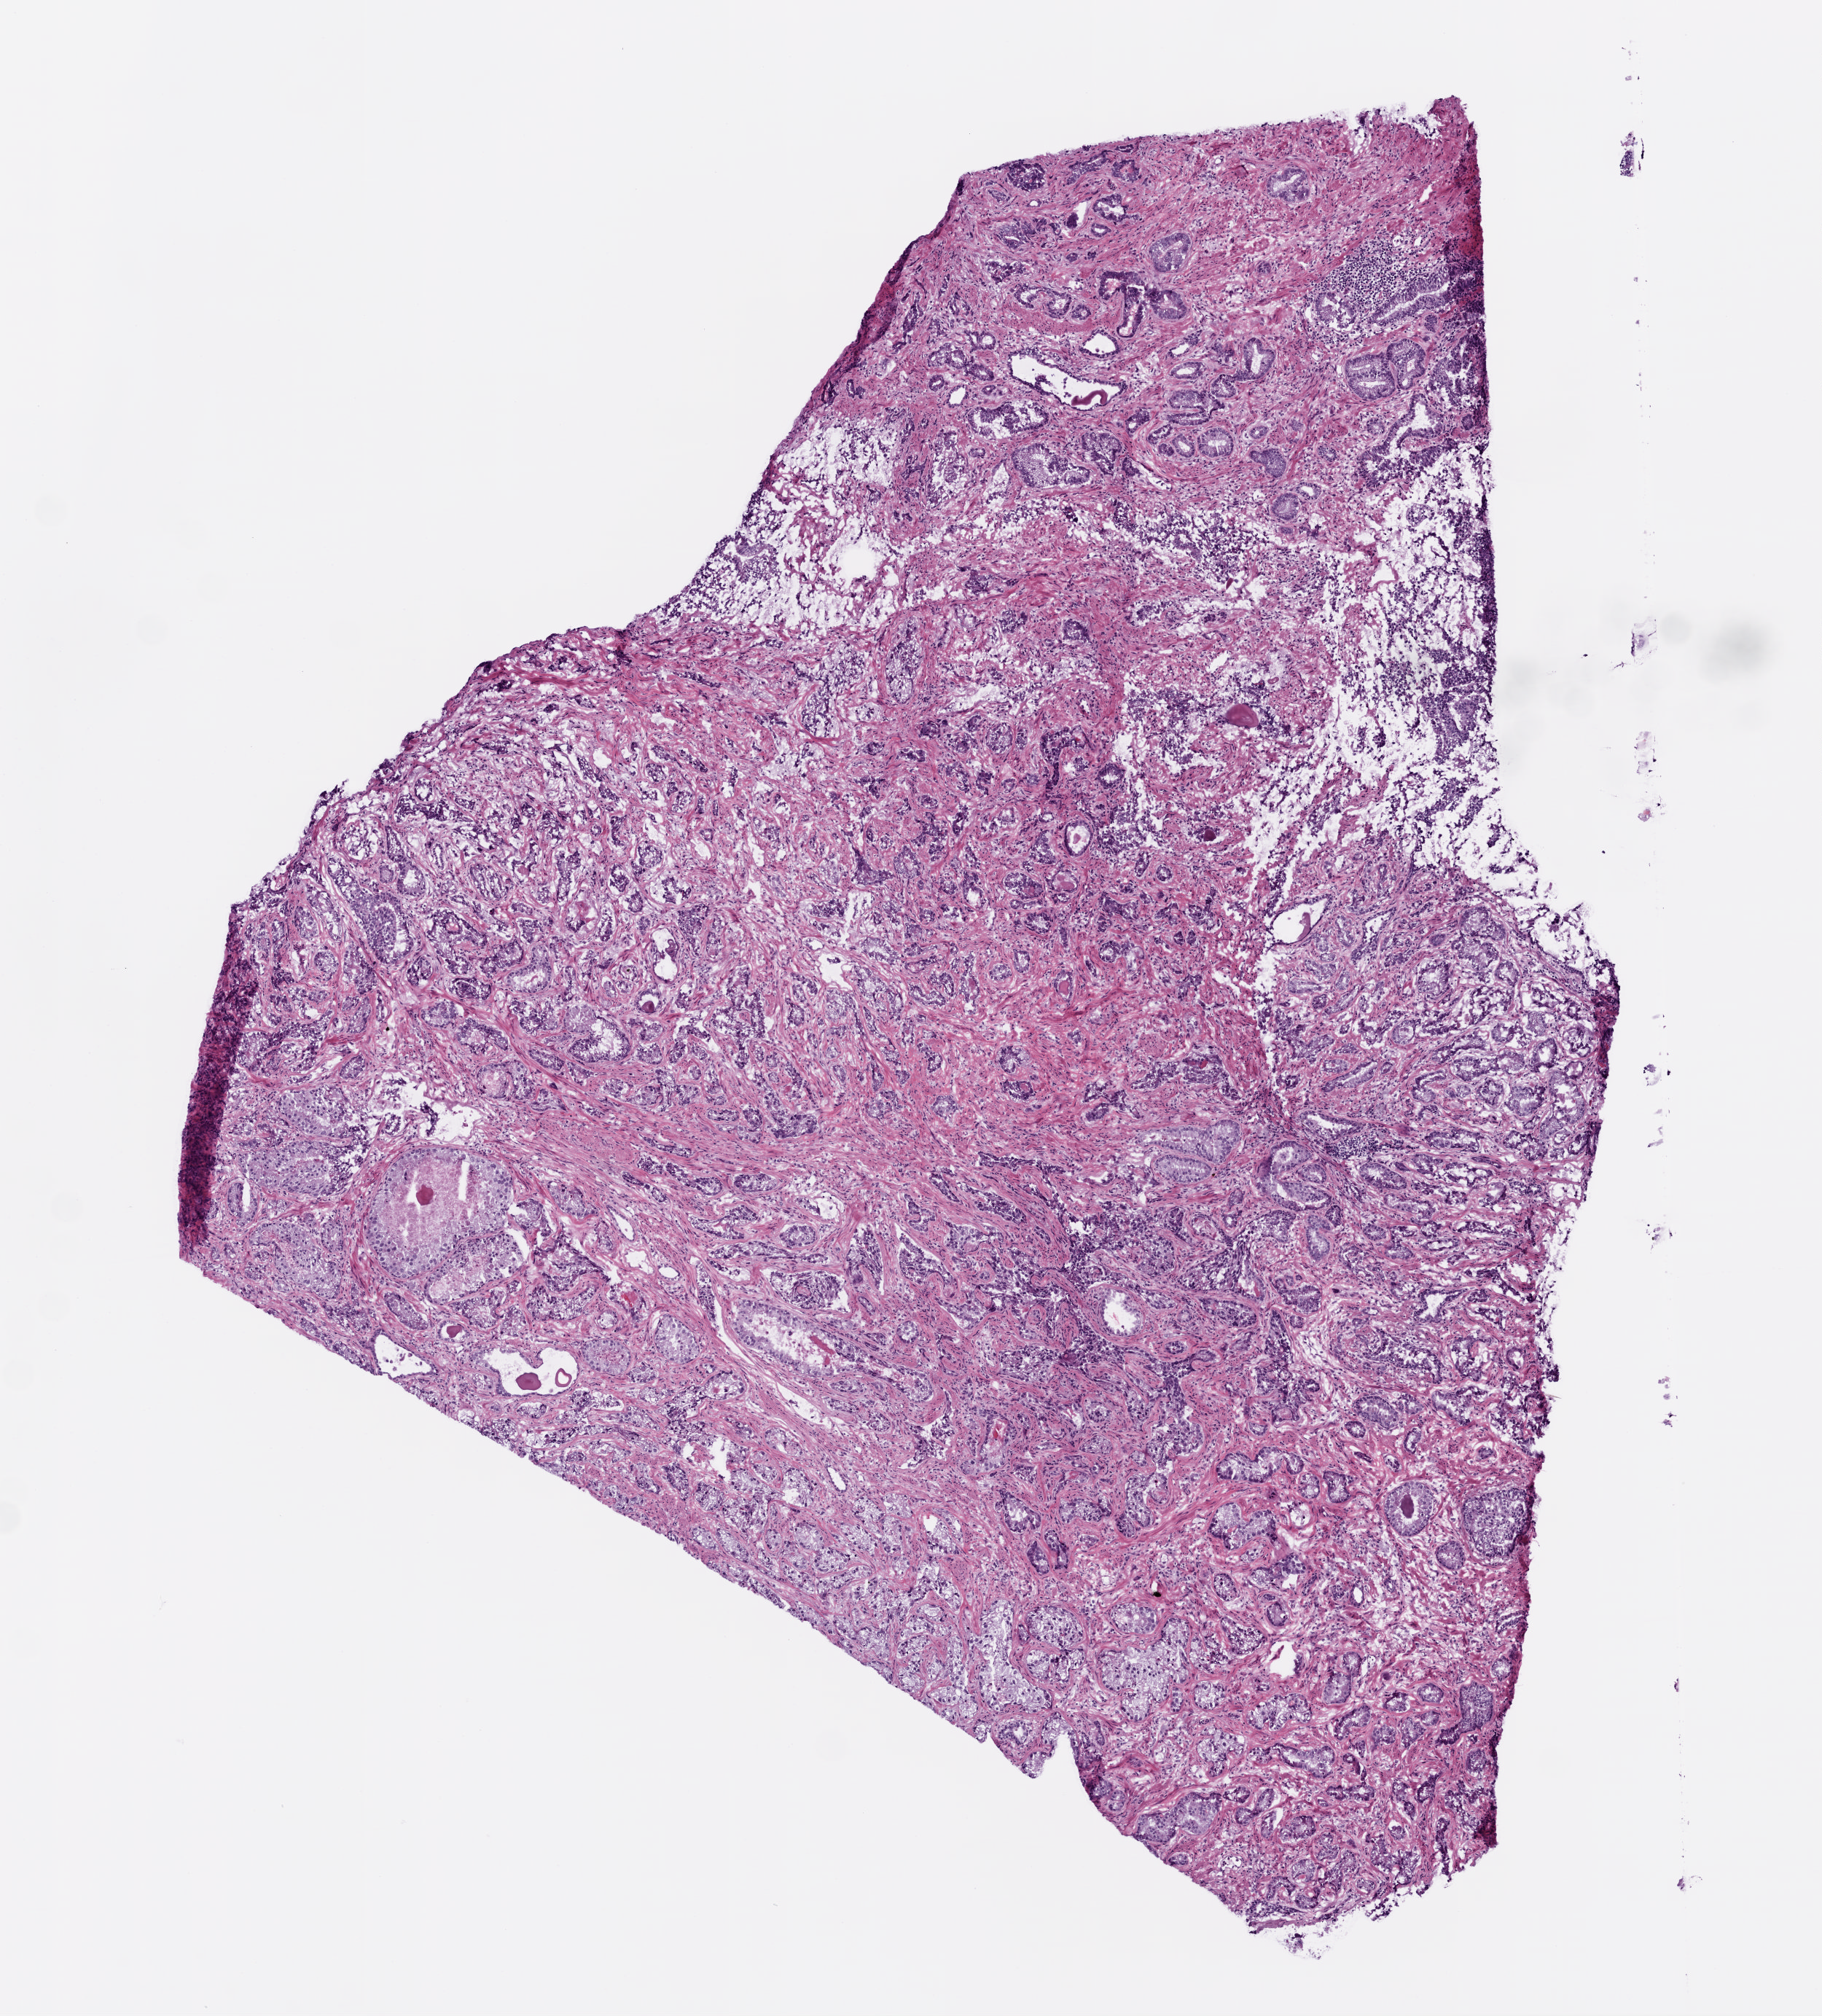
Hematoxylin and eosin (H&E) stained whole-slide image, a low-resolution overview of the entire scanned area, about 5.0 x 5.5 mm (slide scanned at 20x); frozen section from the bottom of the tissue portion; prostate, primary tumour sample. Patient: male, age at initial diagnosis 72 years.
Pathologic diagnosis: Acinar cell carcinoma (prostate gland).